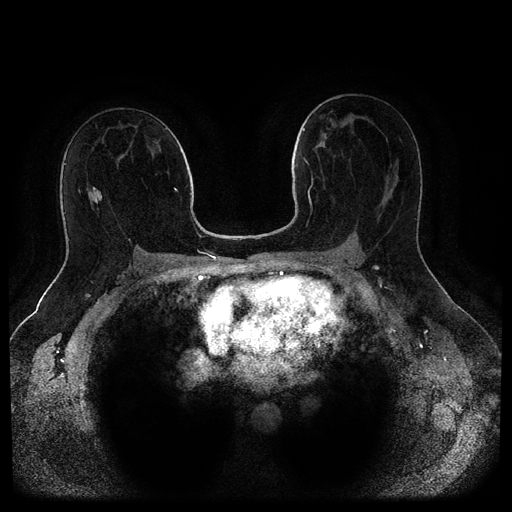
Breast MRI (dynamic contrast-enhanced, multi-phase), one axial slice; slice 55 of 116 in the series (ordered by position); dynamic contrast-enhanced series, time point 2 of 5 at this slice position (early post-contrast); 1.5 T; TE 2.6 ms, TR 5.3 ms; 2 mm slice thickness; 512 × 512 image matrix, field of view 370 × 370 mm. Female patient, age 44 years.
Outlined on this slice (semi-automatic segmentation, software-assisted and operator-edited):
- breast lesion (labelled benign in the annotation): bounding box <90,187,103,204> (left, top, right, bottom; pixels)